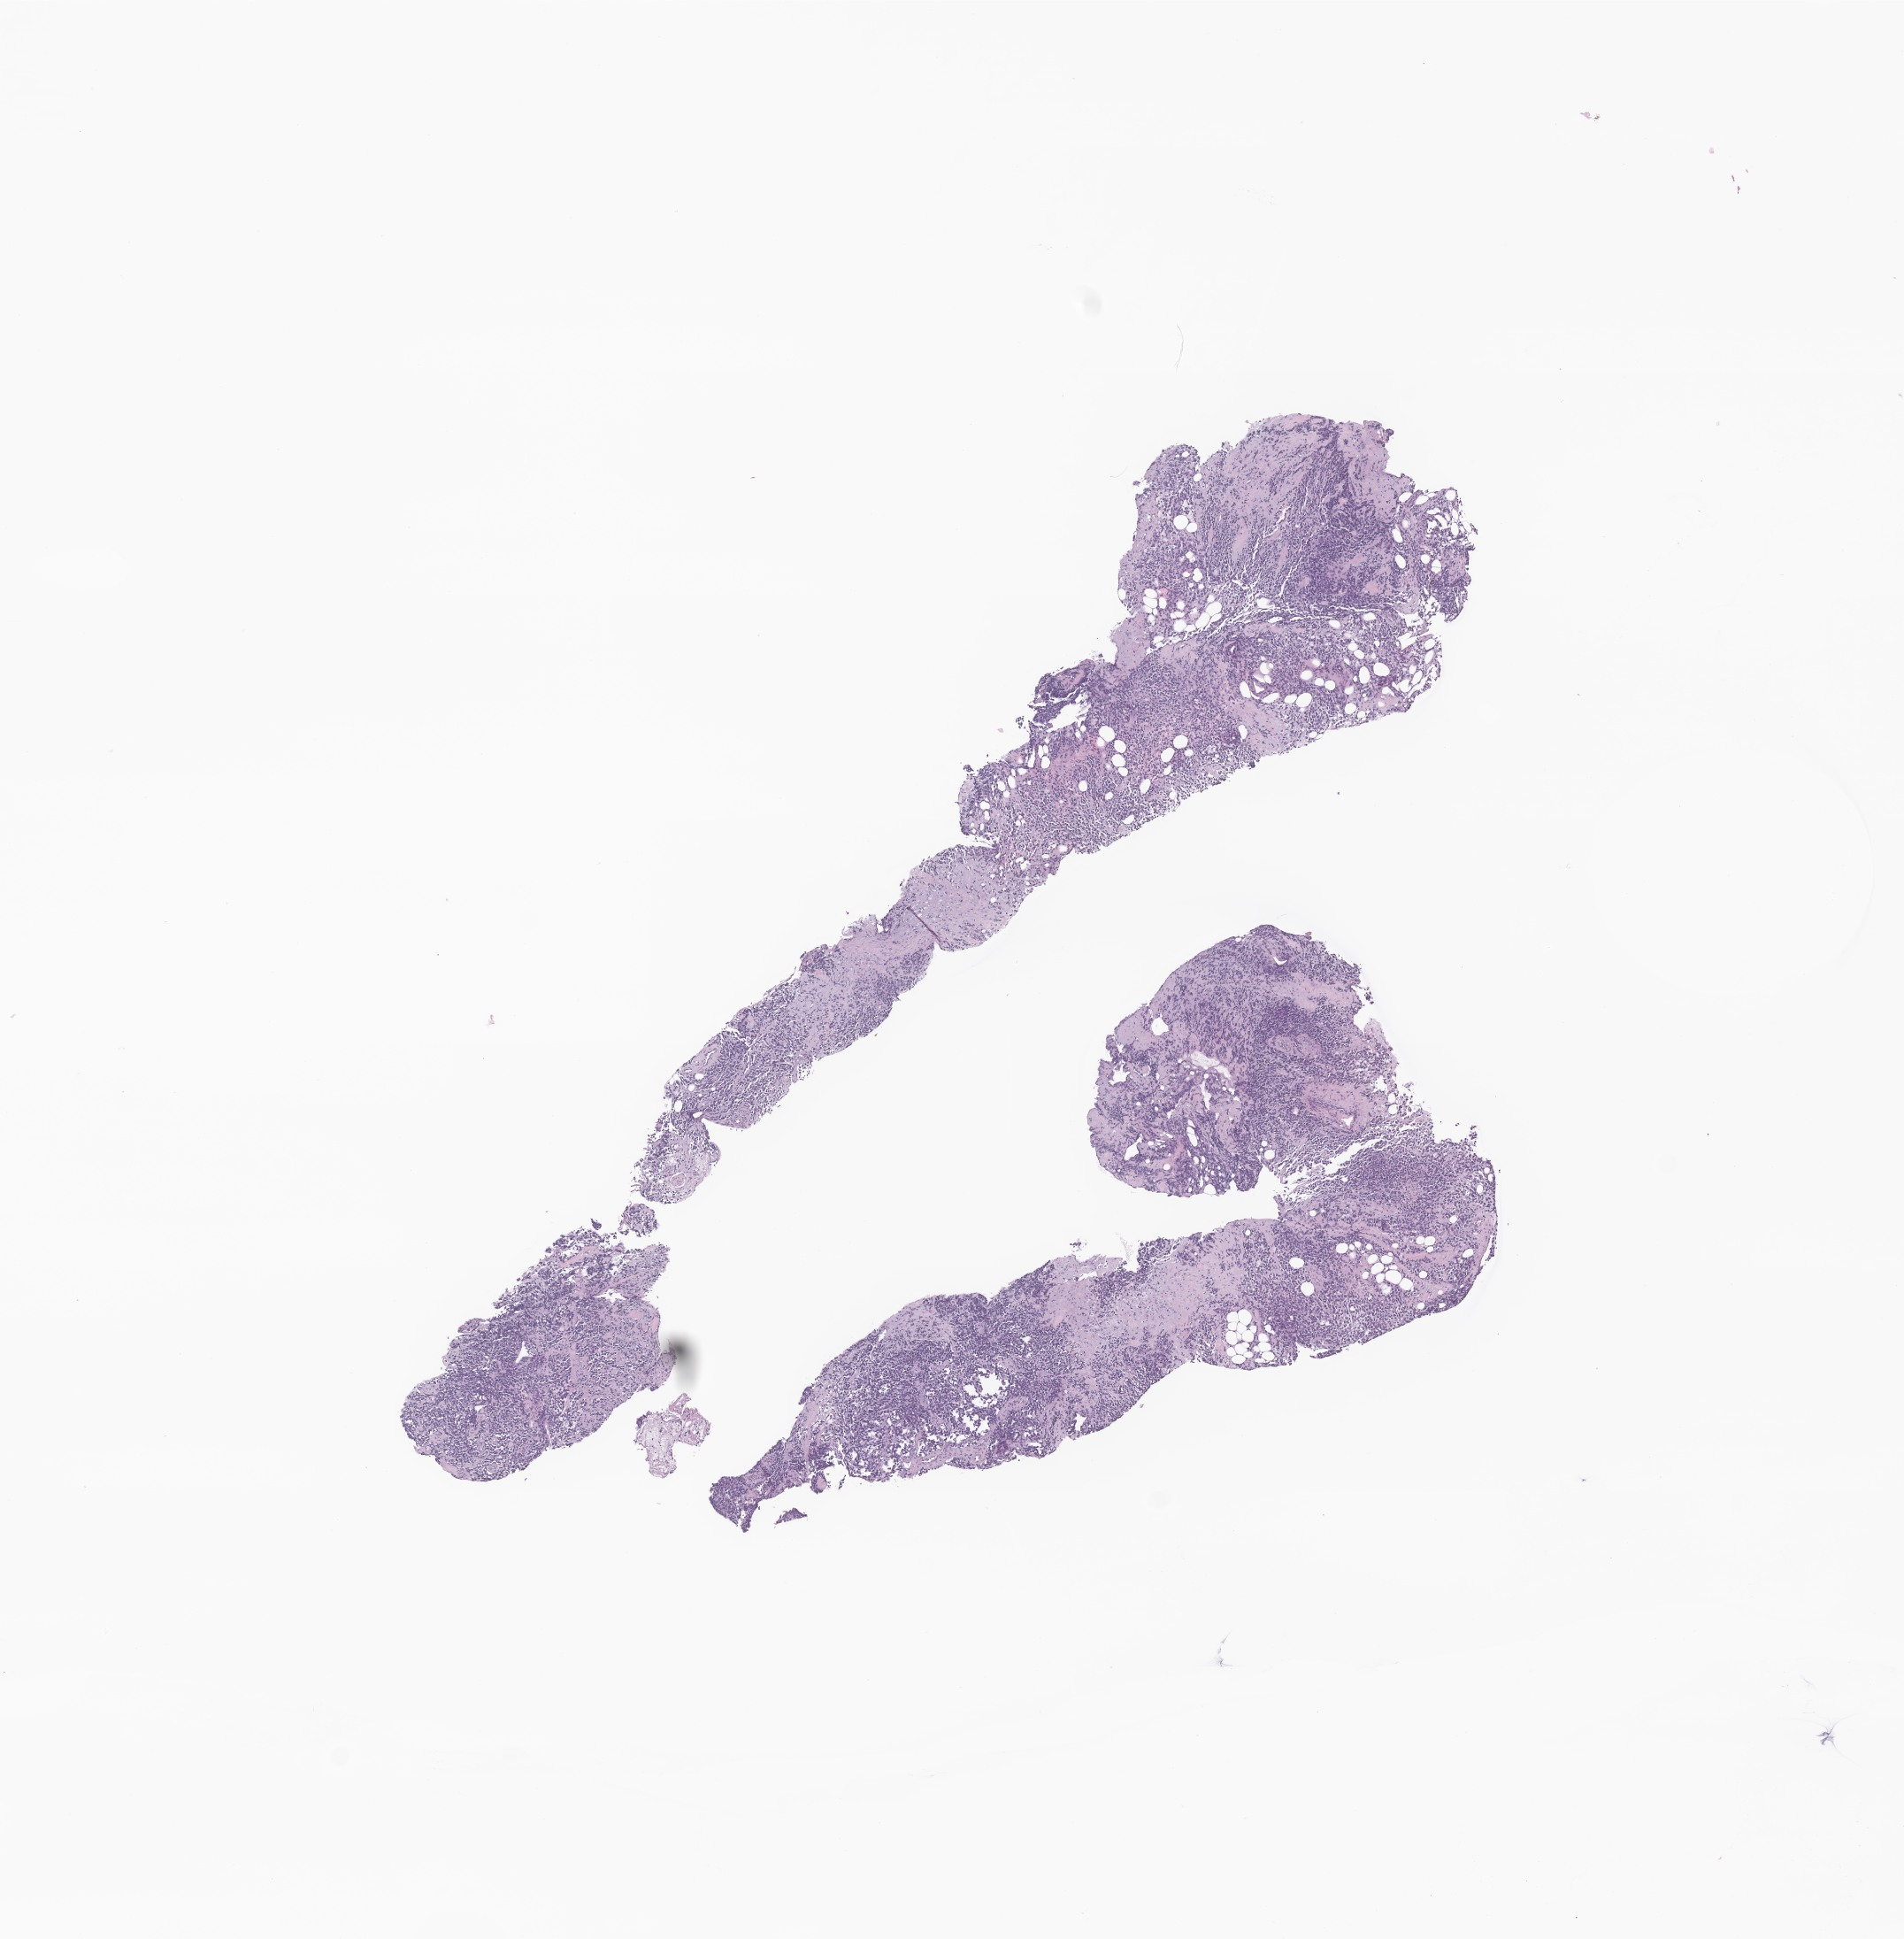
Whole-slide image, haematoxylin and eosin stain of tumor tissue from the prostate — a low-resolution overview of the entire scanned area, about 9.1 x 9.2 mm; FFPE section. Patient male; age 121 months (10 years 1 month).
- recorded diagnosis: Rhabdomyosarcoma, NOS